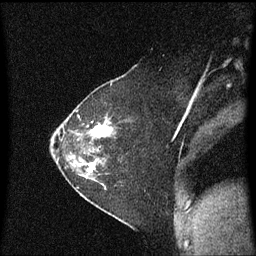
Breast MRI (dynamic contrast-enhanced), one sagittal slice. Slice 38 of 60 in the series (ordered by position). Dynamic contrast-enhanced series, image 2 of 3 at this slice position (ordered by acquisition). 1.5 T. TE 4.2 ms, TR 8.4 ms. 2 mm slice thickness. 256 × 256 image matrix, field of view 200 × 200 mm. Patient: female, 36 years. Case-level facts recorded for this patient, not image findings: setting: breast cancer imaged before/during neoadjuvant chemotherapy; receptor status: HR-positive, HER2-negative.
Outlined on this slice (semi-automatic segmentation, software-assisted and operator-edited):
- analysis volume of interest (the breast-tissue region the enhancement analysis was run in; not a lesion): bounding box <66,102,122,179> (left, top, right, bottom; pixels)
- tumour enhancement mask (voxels above the 70 % enhancement threshold inside the analysis volume of interest): <88,120,113,173>